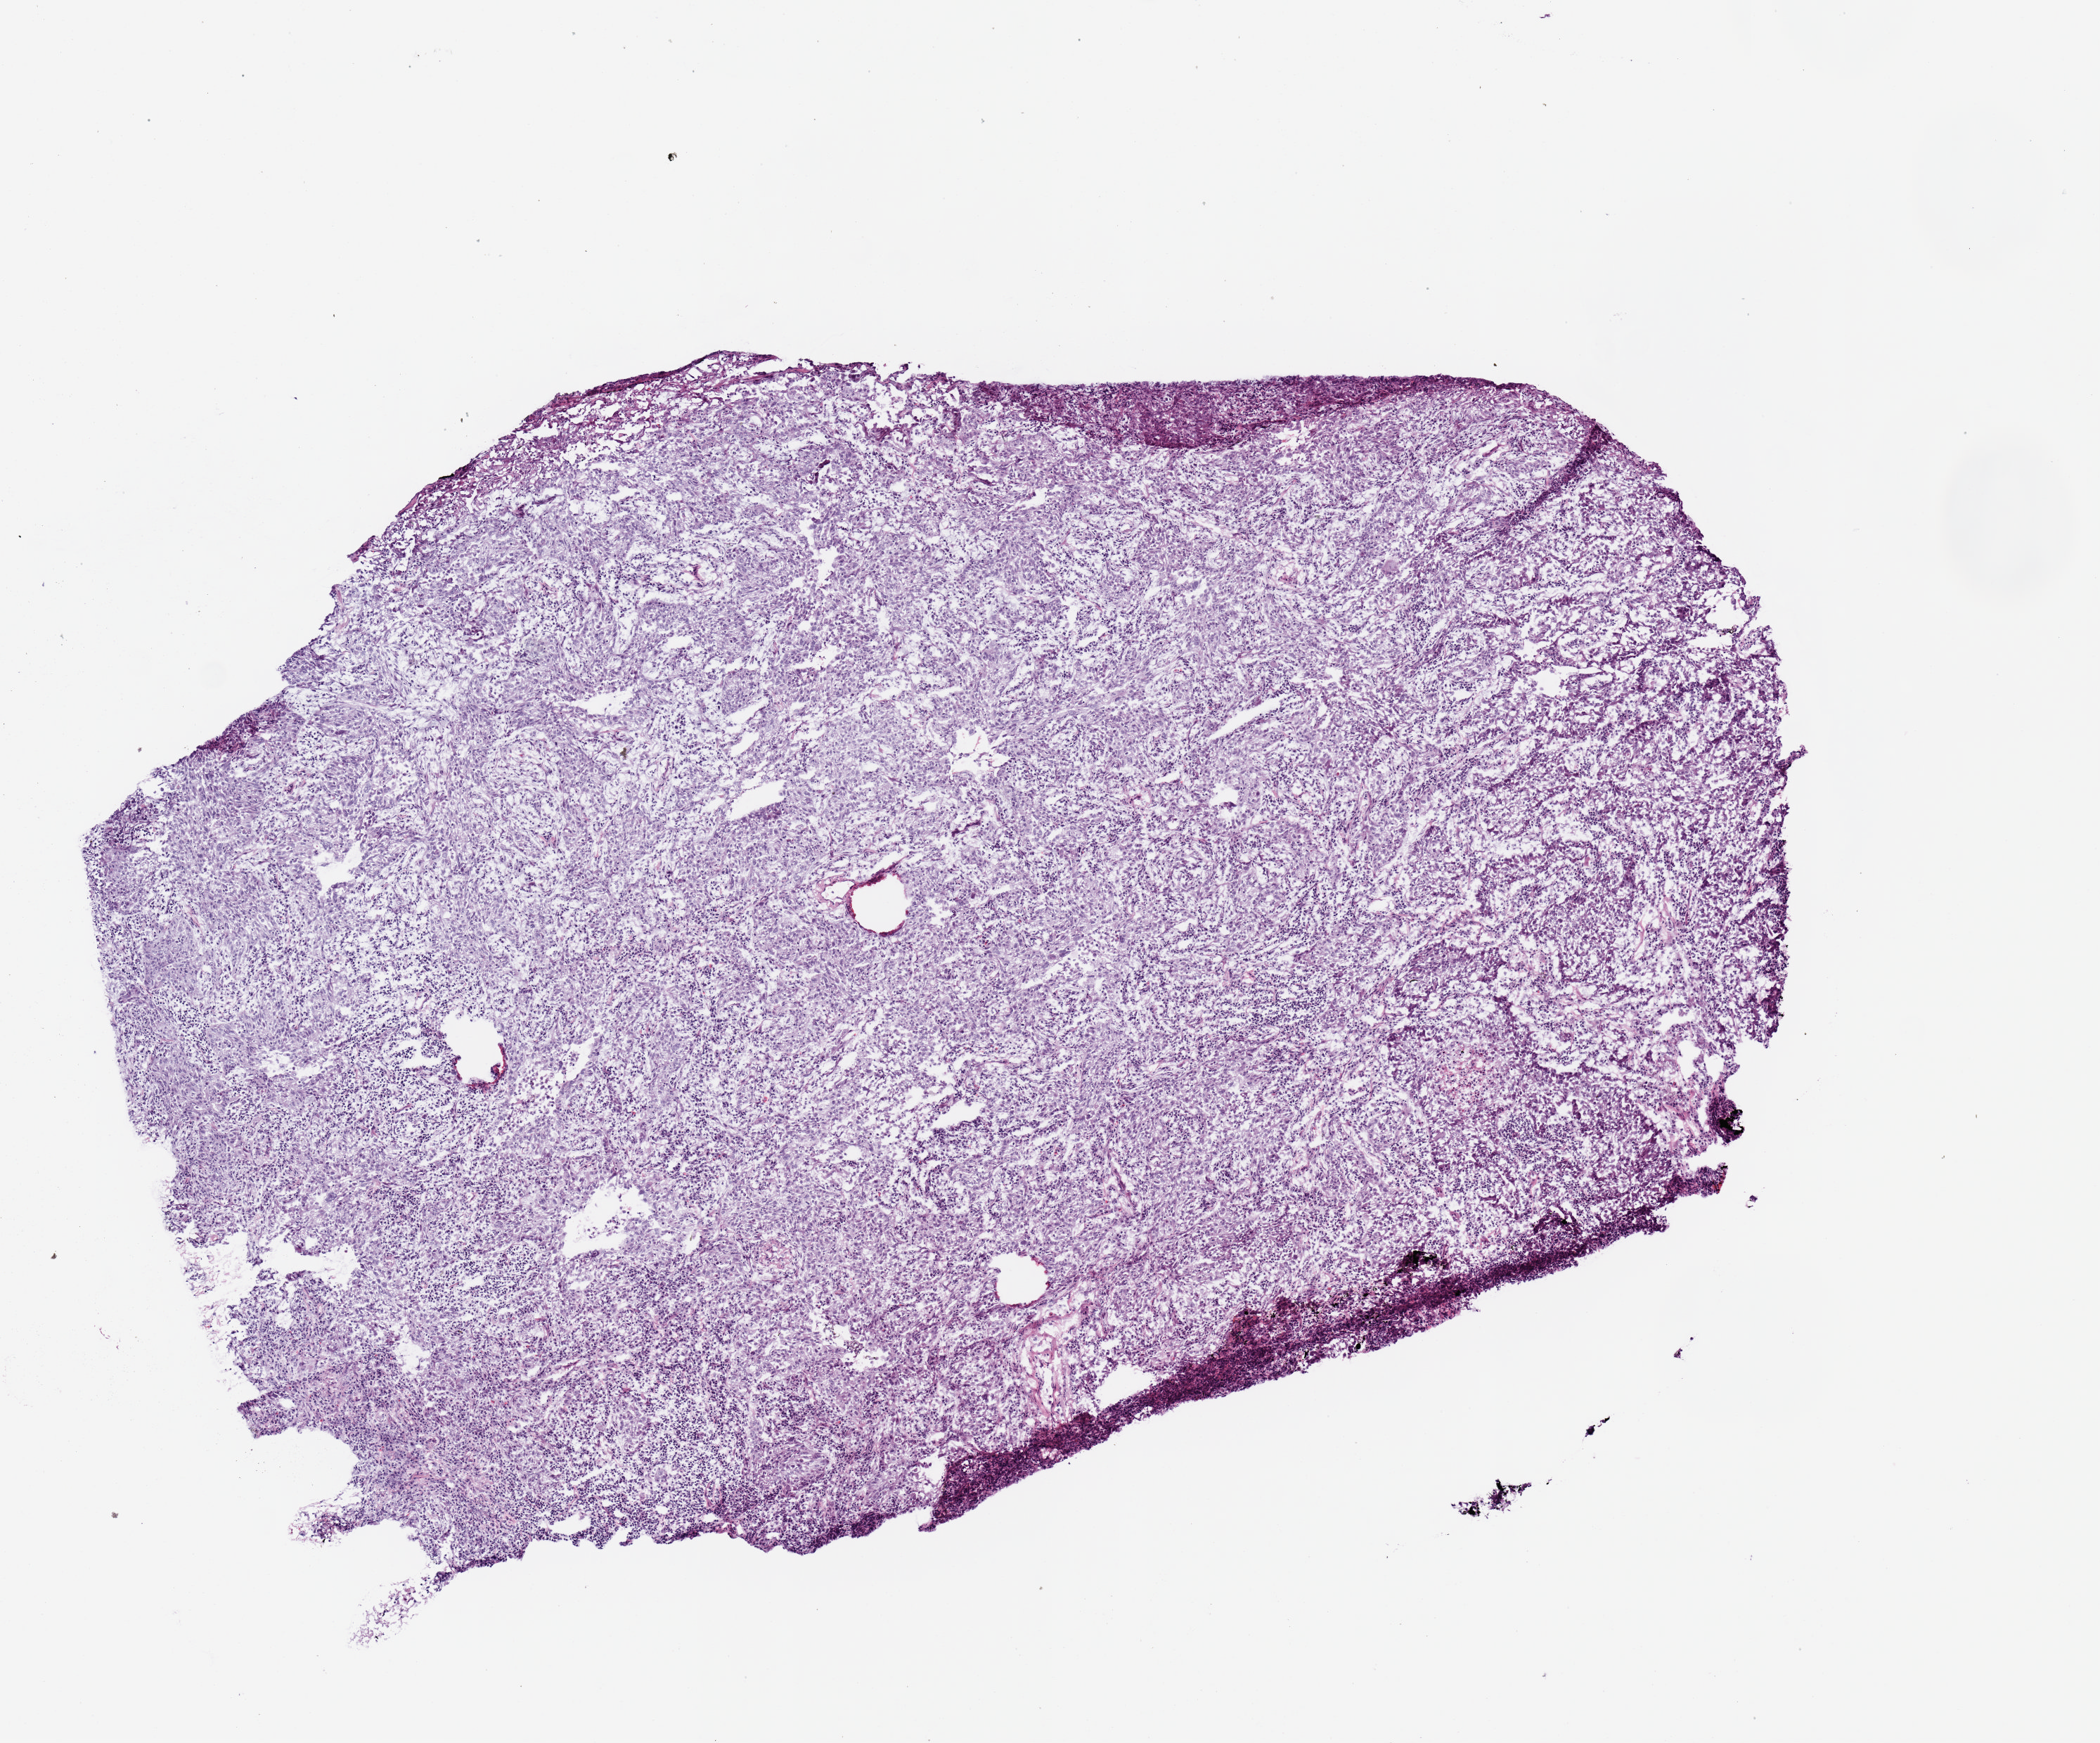
Whole-slide histology image, H&E-stained, shown as a low-resolution overview of the whole scanned area (about 5.9 x 4.9 mm, acquisition: 20x scan), frozen section from the top of the tissue portion, primary tumour sample from the lung. Female, age 75 years at initial diagnosis. Slide review estimates, as recorded: tumour cells 100%, tumour nuclei 61%, normal cells 0%, stromal cells 0%, necrosis 0%. Infiltration values recorded for this section: lymphocyte infiltration 30%, monocyte infiltration 2%, neutrophil infiltration 2%.
• diagnosis: Adenocarcinoma, NOS (lower lobe, lung)
• TNM: T1a N0 MX
• AJCC pathologic stage: IA (7th edition)
• laterality: left